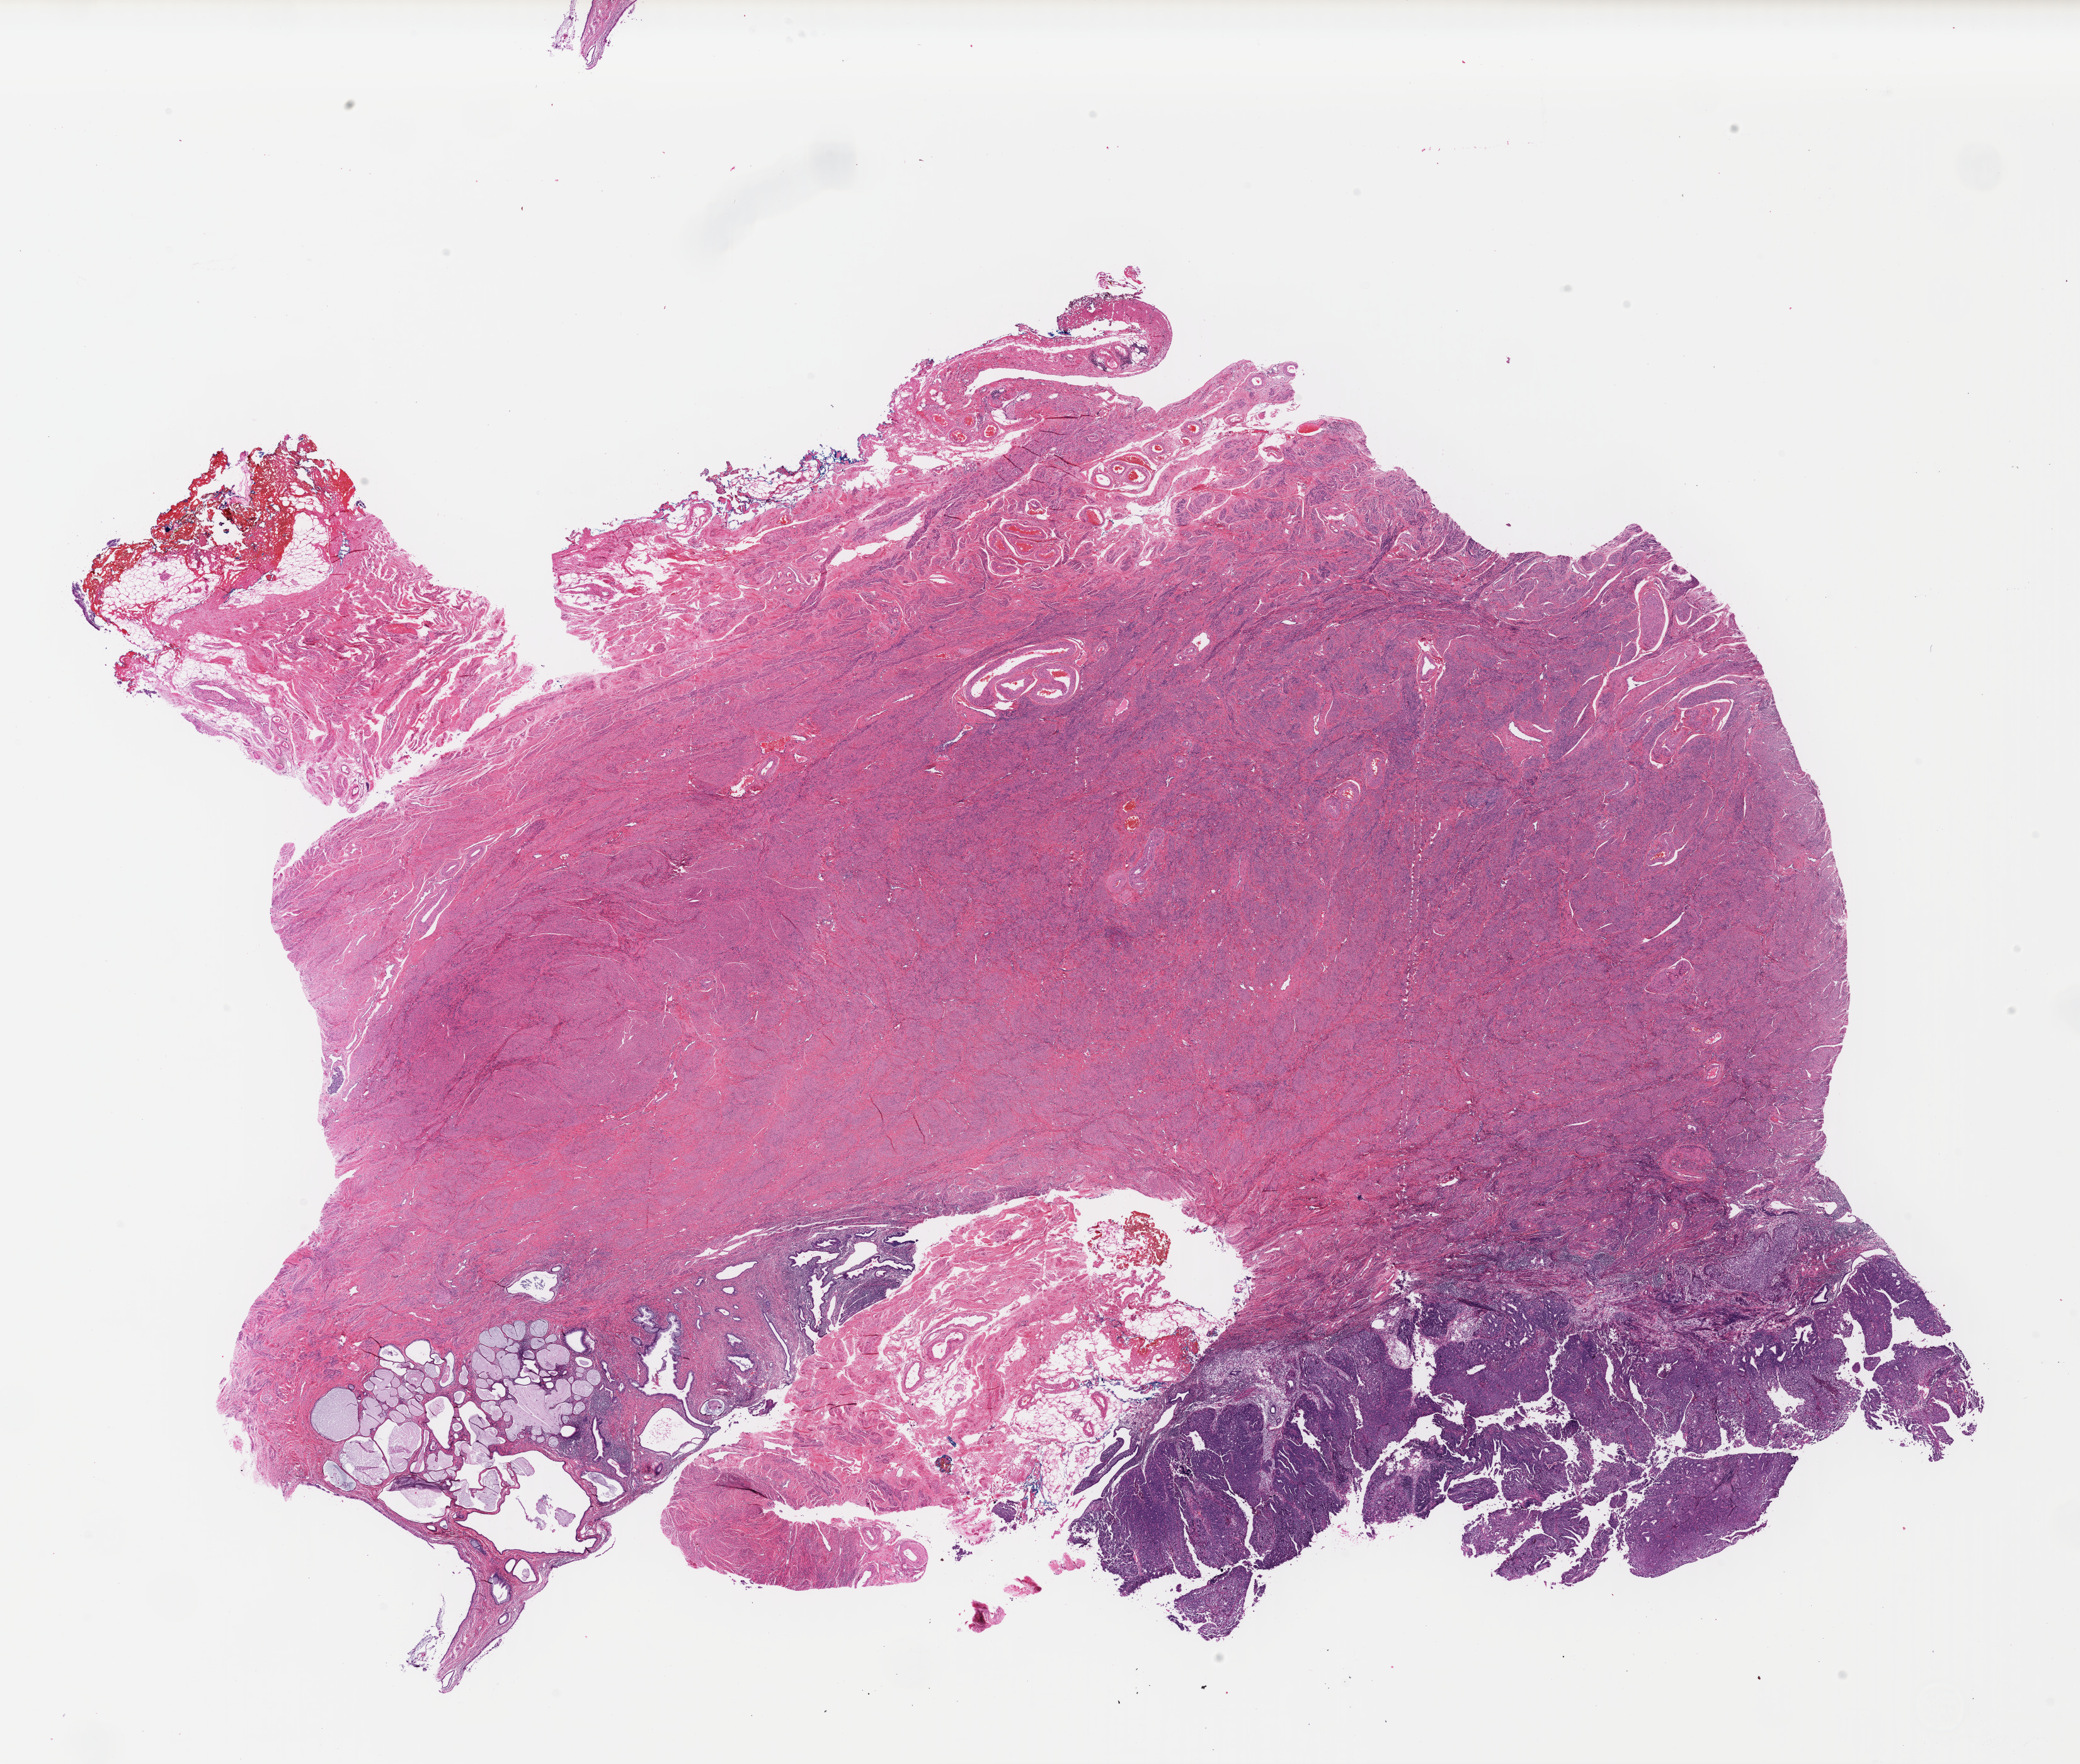
H&E whole-slide image — a low-resolution overview of the entire scanned area, about 26.0 x 22.0 mm (acquisition: 40x scan), formalin-fixed paraffin-embedded (FFPE) diagnostic section, uterus, primary tumour sample. Female patient; age at initial diagnosis 73 years. Histologic grade: G3 (poorly differentiated).
- FIGO stage: IC
- pathologic diagnosis: Endometrioid adenocarcinoma, NOS
- lymph nodes positive (case pathology): 0 of 2 examined